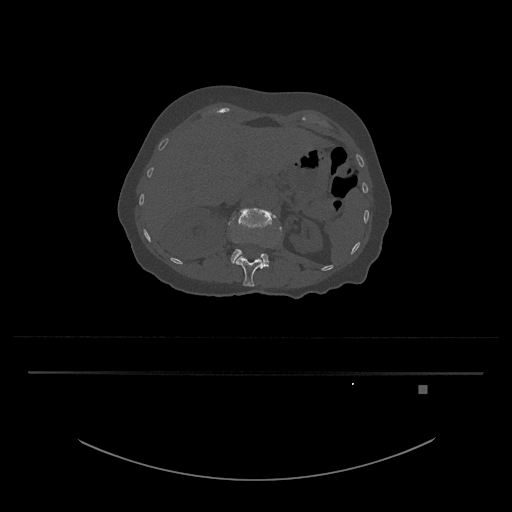
CT including the spine, one axial slice. Position 529 of 797 along the scan axis. 120 kVp. Bone window (W 1800 / L 400 HU). 0.5 mm slice thickness. 512 × 512 image matrix, field of view 500 × 500 mm. Patient: female, 57 years. From the clinical record (not read from this slice): primary cancer: cervical.
Annotated regions visible in this slice (semi-automatically segmented with operator editing):
- L1 vertebra: bounding box [x1, y1, x2, y2] px = [233, 226, 282, 287]